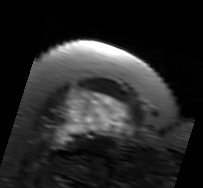
MRI of an extremity soft-tissue mass, one axial slice; slice 61 of 91 in the series (ordered by position); T2-weighted fat-saturated; MR volume resampled by the dataset authors to the PET/CT grid (not the native acquisition matrix); 203 × 188 image matrix, field of view 198 × 184 mm. Female patient. Case-level facts recorded for this patient, not image findings: histological type: malignant solitary fibrous tumor; grade: intermediate; site of the primary tumour: right thigh.
Structures marked on this image (expert contour drawn on MRI and transferred to this co-registered scan by the dataset authors):
- gross tumour volume including surrounding oedema: bounding box <53,86,130,148> (left, top, right, bottom; pixels)
- gross tumour volume (mass): <56,90,130,143>